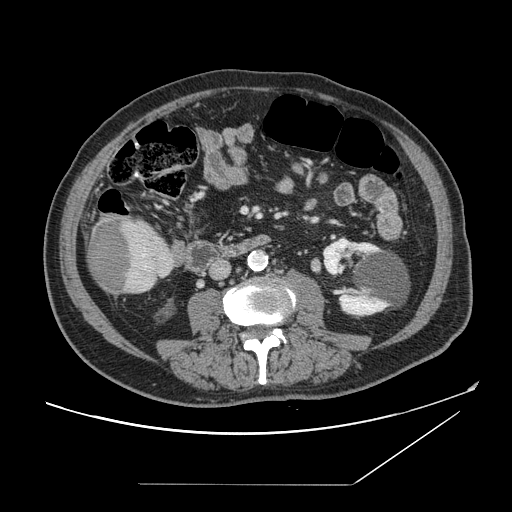
Contrast-enhanced abdominal CT, one axial slice; slice 37 of 166 in the series (ordered by position); intravenous contrast given; soft-tissue window (W 400 / L 40 HU); 2.5 mm slice thickness; 512 × 512 image matrix, field of view 416 × 416 mm. Male patient, age 80 years. Case-level facts recorded for this patient, not image findings: diagnosis: colorectal cancer liver metastases, imaged before liver resection; multiple liver metastases: no; largest metastasis: 2.2 cm; disease in both lobes: no.
Annotated regions visible in this slice (manually delineated by an expert):
- liver: bounding box <88,214,175,294> (left, top, right, bottom; pixels)
- liver metastasis: <91,220,133,292>